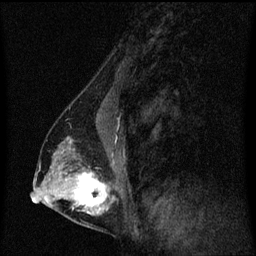
Breast MRI (dynamic contrast-enhanced), one sagittal slice. Position 32 of 60 along the scan axis. Dynamic contrast-enhanced series, image 2 of 3 at this slice position (ordered by acquisition). 1.5 T. TE 4.2 ms, TR 8.4 ms. 256 × 256 image matrix, field of view 200 × 200 mm. Patient: female, 40 years. From the clinical record (not read from this slice): setting: breast cancer imaged before/during neoadjuvant chemotherapy; receptor status: triple-negative.
Annotated regions visible in this slice (semi-automatically segmented with operator editing):
- analysis volume of interest (the breast-tissue region the enhancement analysis was run in; not a lesion): bounding box [x1, y1, x2, y2] px = [44, 128, 117, 221]
- tumour enhancement mask (voxels above the 70 % enhancement threshold inside the analysis volume of interest): [74, 172, 107, 215]